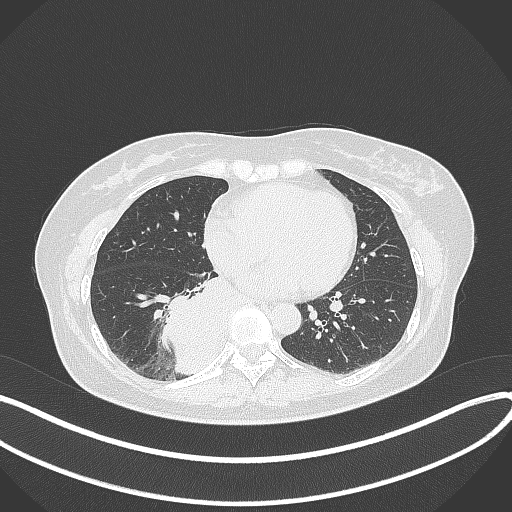
Chest CT, one axial slice. Position 137 of 331 along the scan axis. Lung window (W 1500 / L -600 HU). 1 mm slice thickness. 512 × 512 image matrix, field of view 400 × 400 mm. Patient: female, 54 years. Case-level facts recorded for this patient, not image findings: clinical TNM (as recorded): T4 N0 M0.
Structures marked on this image (bounding box drawn by a radiologist):
- lung tumour (recorded histology: adenocarcinoma): bounding box (x1, y1, x2, y2) in pixels: (159, 282, 236, 370)